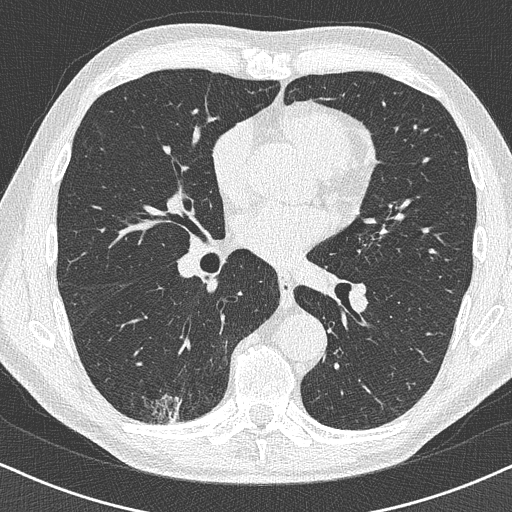
Axial slice from a low-dose chest CT screening exam, baseline screening round, lung window (W 1500 / L -600 HU), 1 mm slice thickness, 120 kVp, 512 × 512 image matrix, field of view 320 × 320 mm. Male participant, aged 63 years at enrolment. Former smoker at enrolment.
Expert reader's lesion annotation, bounding box (x1, y1, x2, y2) in pixels: (131, 363, 203, 429). Screening reader's record for this exam (one nodule recorded; not confirmed to be the boxed lesion): non-calcified nodule or mass ≥4 mm, right lower lobe, 16 × 13 mm, poorly defined margins. Participant outcome: lung cancer diagnosed 74 days after this screen — adenocarcinoma, NOS, right lower lobe, moderately differentiated (G2), stage IA (AJCC 6th edition), 20 mm at pathology.